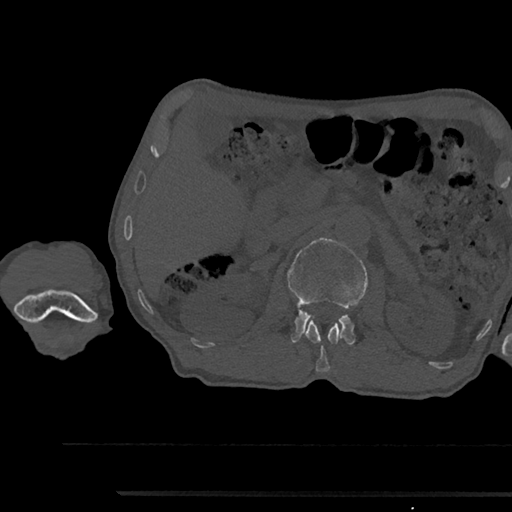
CT including the spine, one axial slice. Position 599 of 797 along the scan axis. Reconstruction kernel Br40s/3. 120 kVp. Bone window (W 1800 / L 400 HU). 0.5 mm slice thickness. 512 × 512 image matrix, field of view 367 × 367 mm. Male patient, age 79 years. Case-level facts recorded for this patient, not image findings: primary cancer: prostate.
Annotated regions visible in this slice (semi-automatically segmented with operator editing):
- L1 vertebra: bounding box (x1, y1, x2, y2) in pixels: (305, 320, 343, 372)
- L2 vertebra: (288, 238, 368, 345)